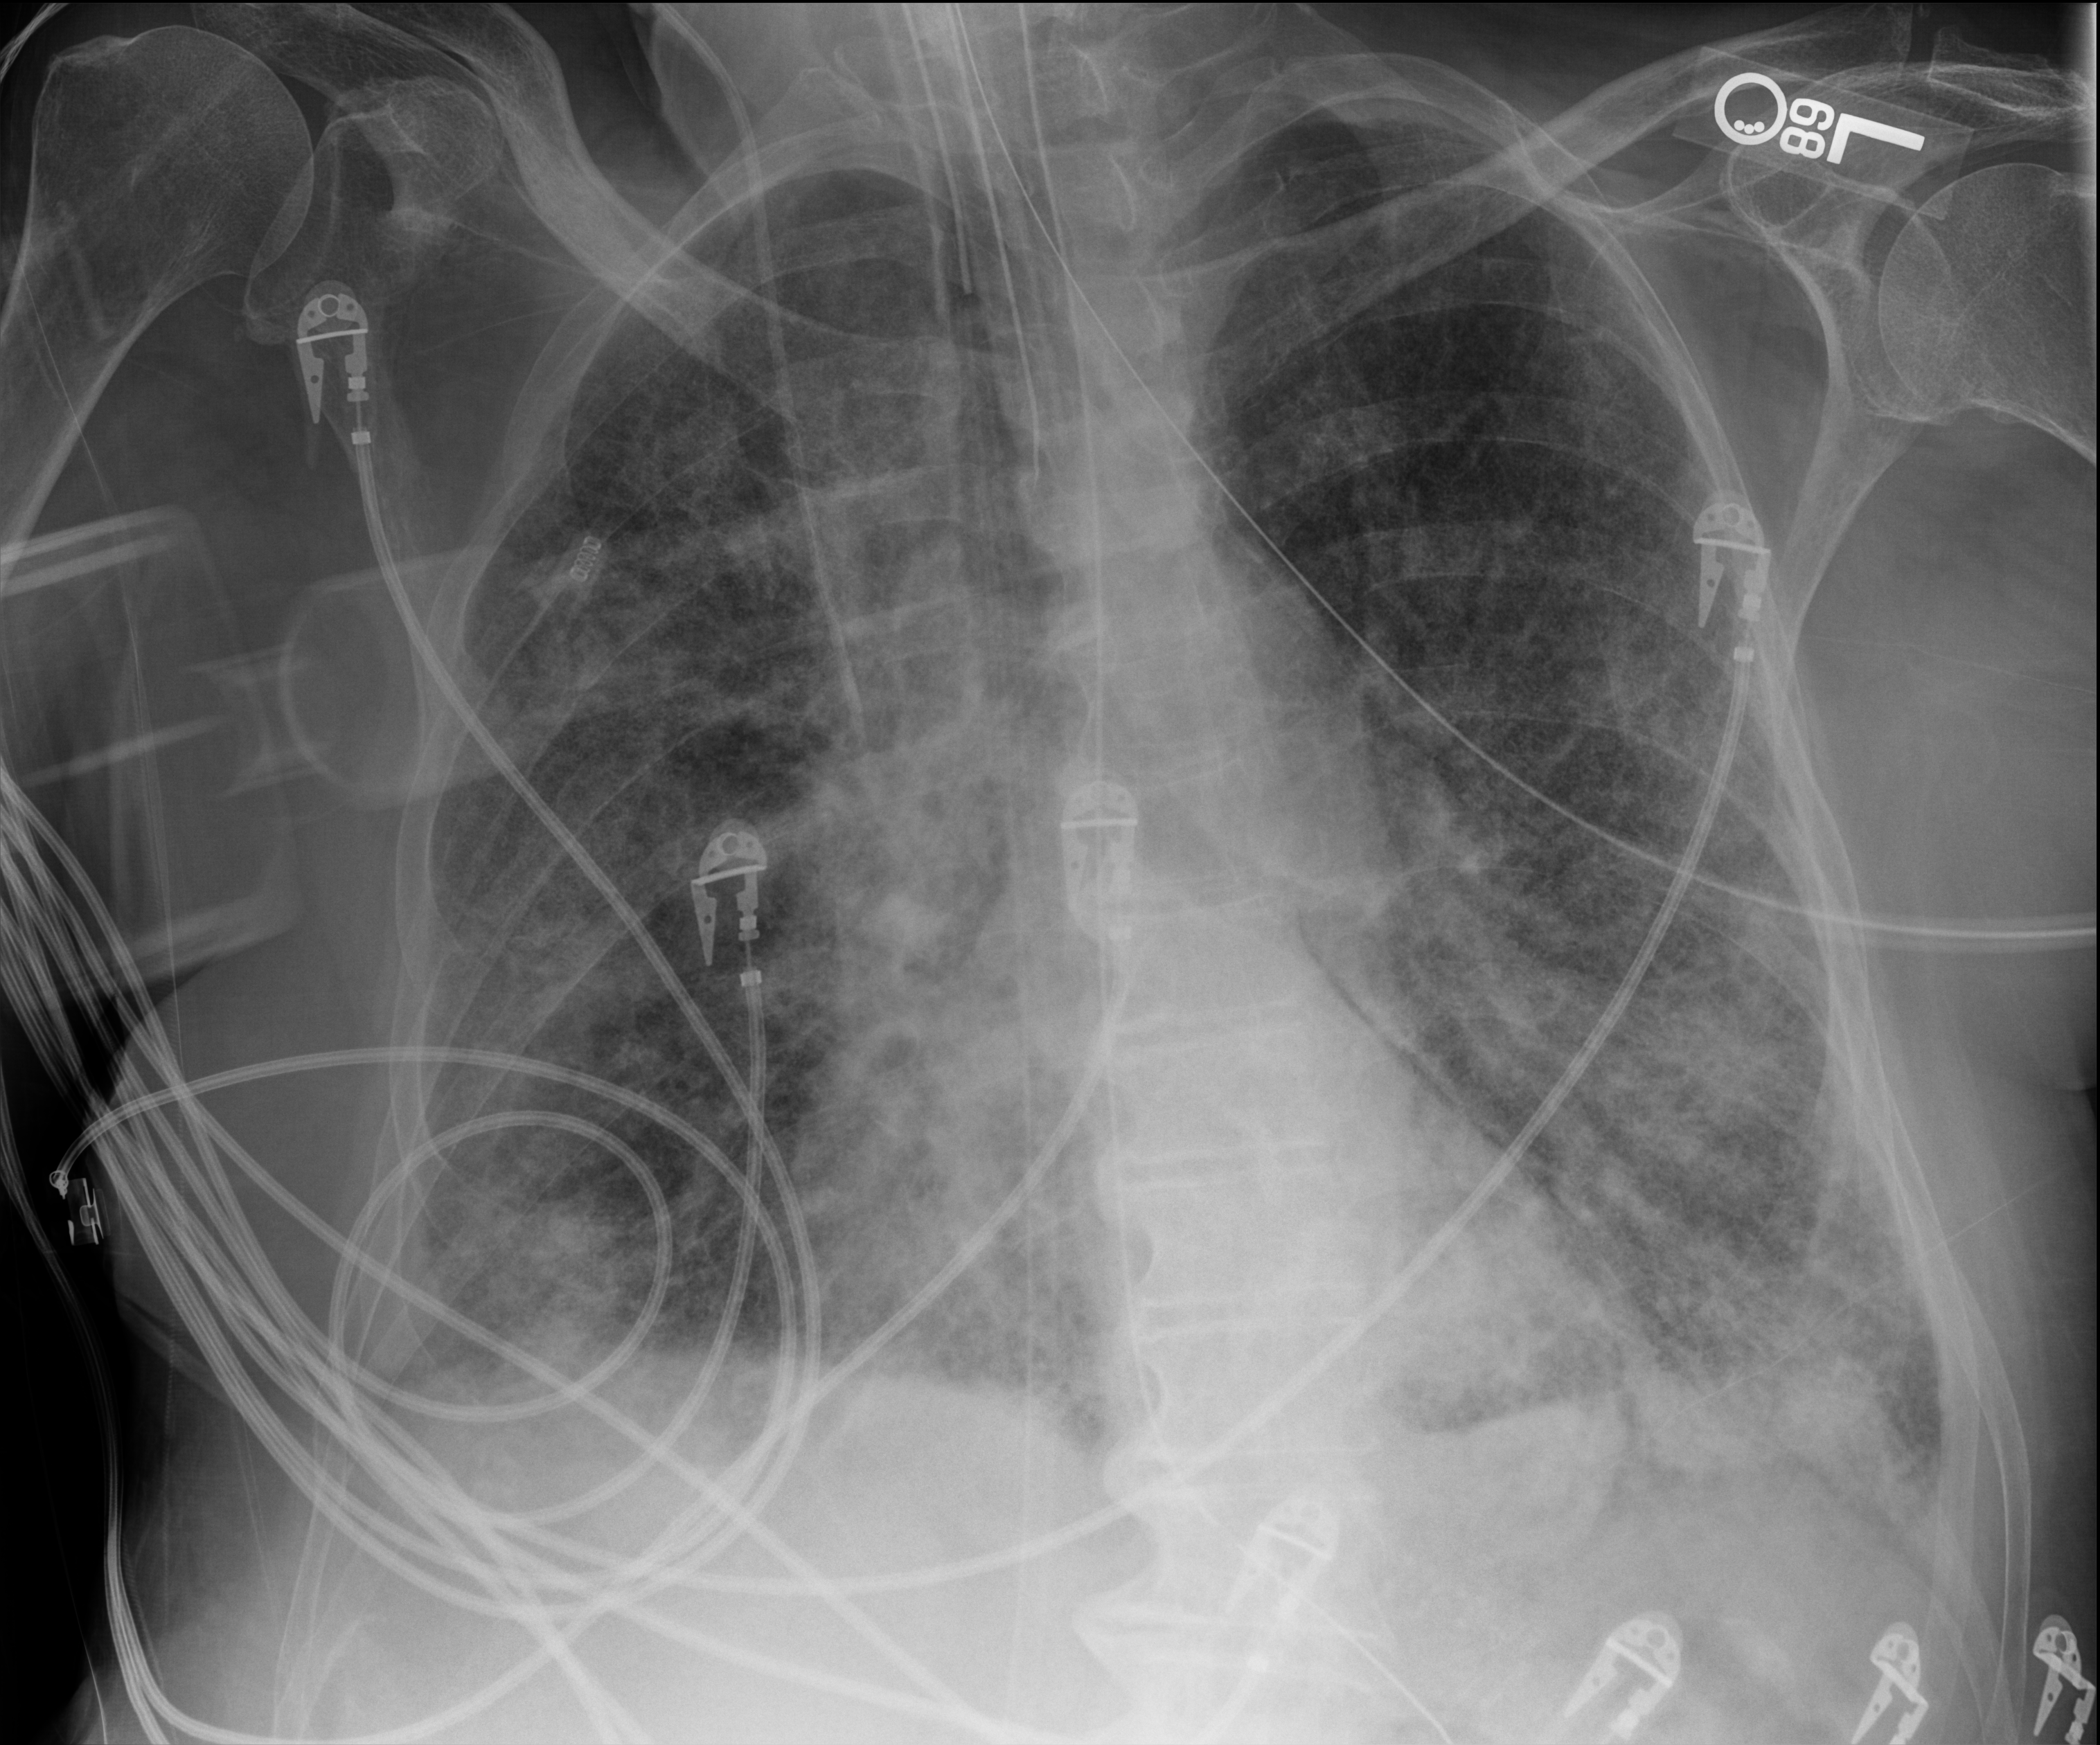
Chest X-ray (portable); anteroposterior (AP) projection. Male patient hospitalised with COVID-19, age 75–90 years.
Hospital-stay facts (about this admission, not read from this image; timing relative to this image not recorded): chronic kidney disease (admission record): no; mechanically ventilated during this hospital stay: yes; admitted to intensive care during this hospital stay: yes.